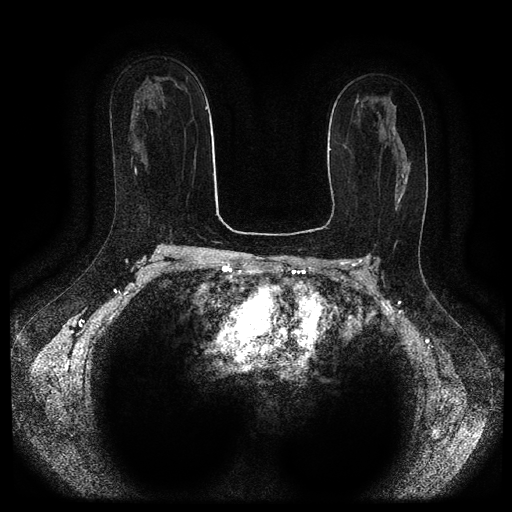
Breast MRI (dynamic contrast-enhanced, multi-phase), one axial slice; slice 61 of 116 in the series (ordered by position); dynamic contrast-enhanced series, time point 2 of 5 at this slice position (early post-contrast); 1.5 T; TE 2.7 ms, TR 5.4 ms; 2 mm slice thickness; 512 × 512 image matrix. Patient: female, 47 years.
Structures marked on this image (semi-automatically segmented with operator editing):
- breast lesion (labelled benign in the annotation): bounding box (x1, y1, x2, y2) in pixels: (392, 126, 396, 139)